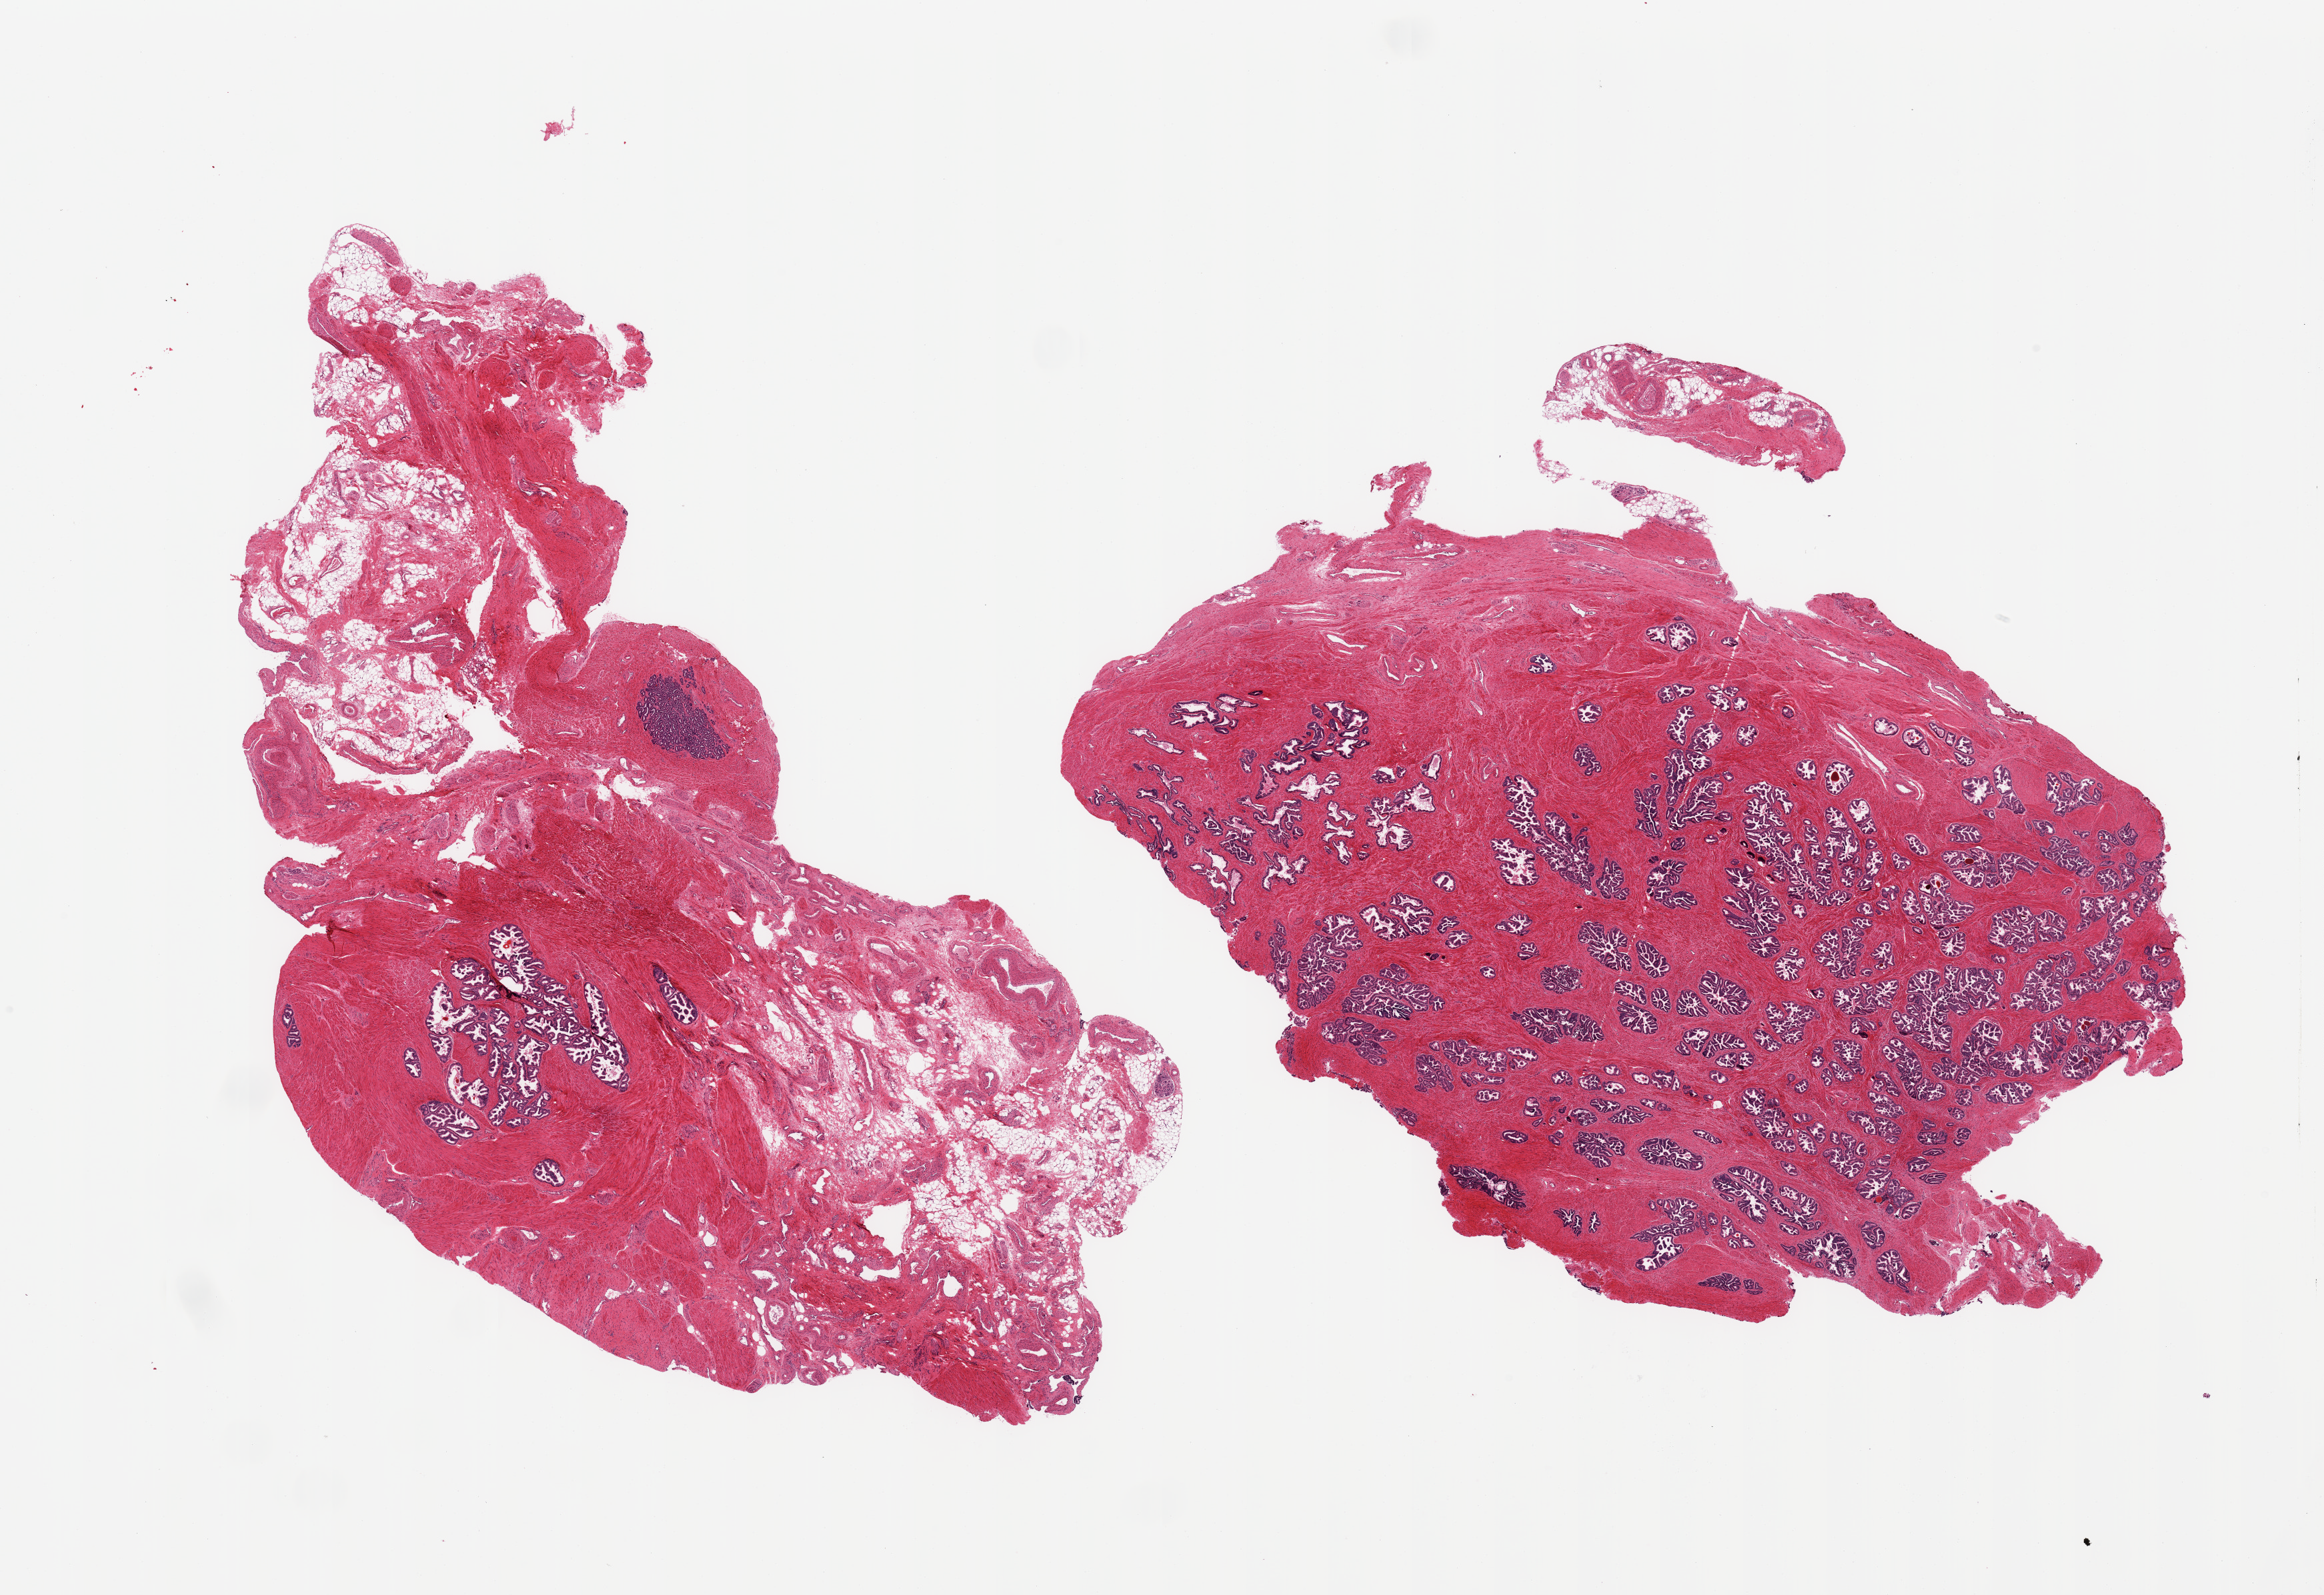
Digitized haematoxylin and eosin-stained section, brightfield, whole scanned area (about 27.6 x 18.9 mm, from a 20x scan) shown as a low-resolution overview, PAXgene-fixed paraffin-embedded (PFPE) section, section of prostate (target tissue), donor tissue sample.
• review note (as recorded): 2 pieces, no abnormalities; ~1mm focus seminal vesicle